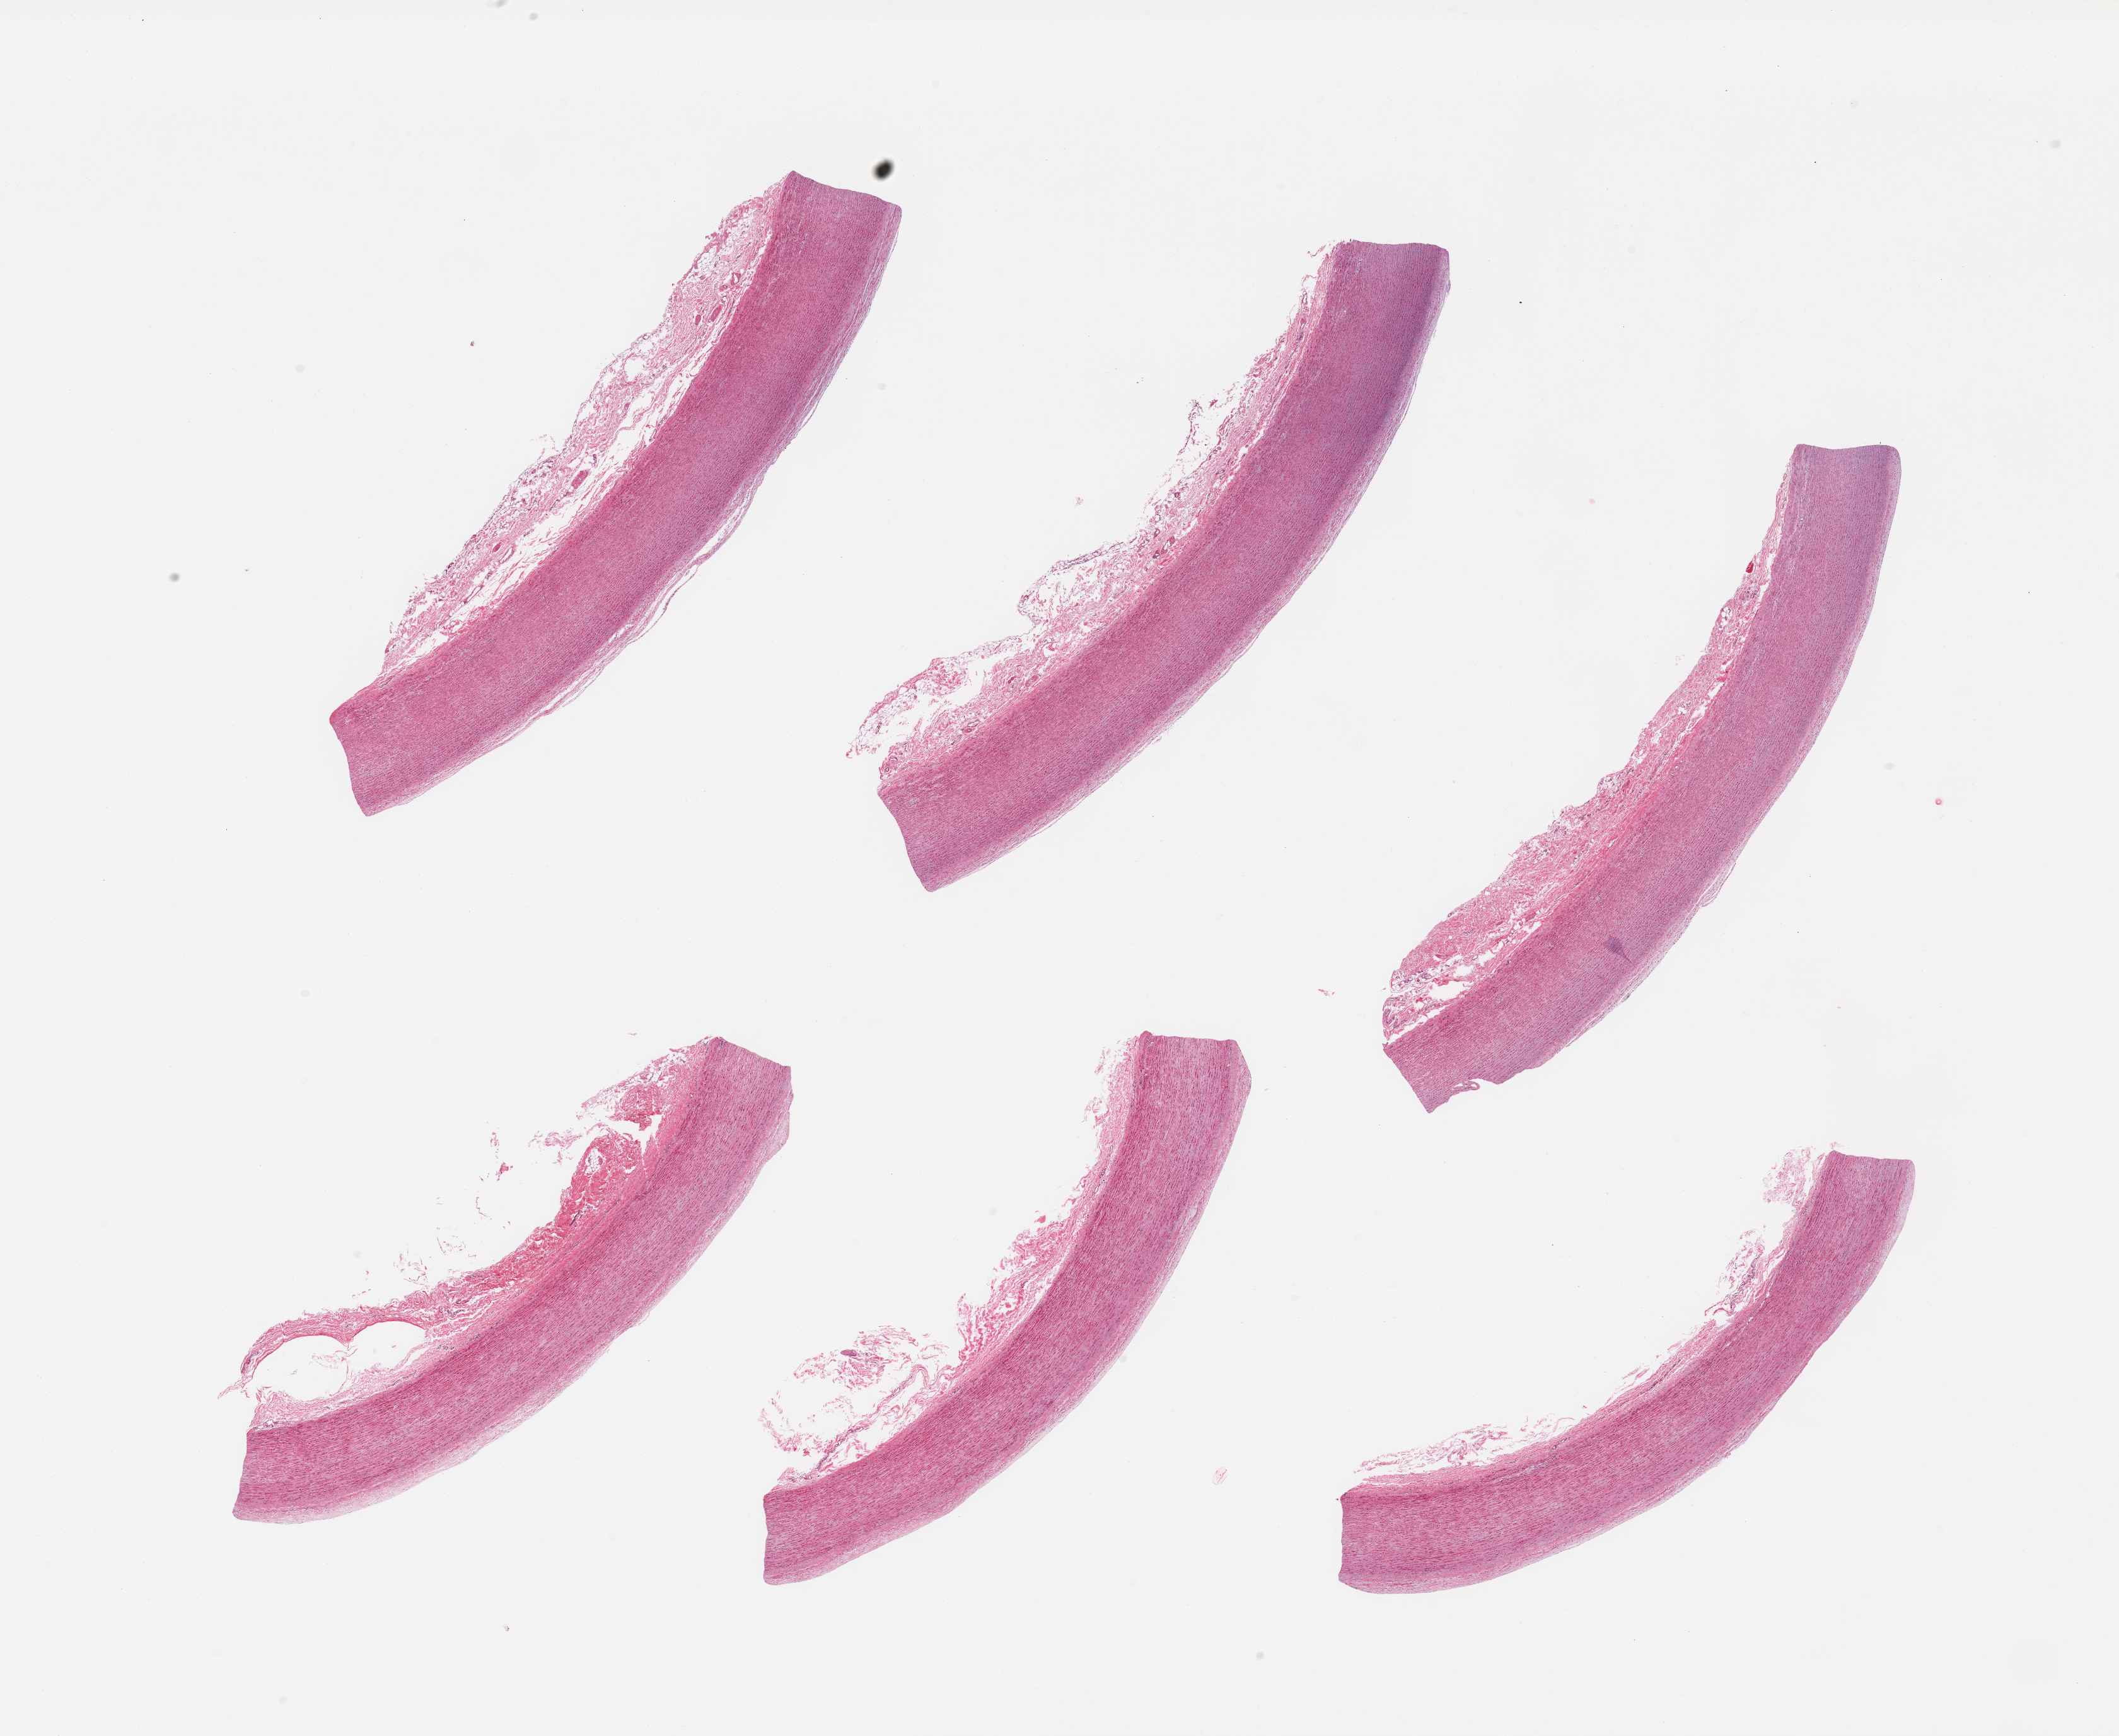
Digitized H&E-stained section, brightfield — low-resolution overview of the scanned area, about 26.6 x 21.8 mm. PAXgene-fixed paraffin-embedded (PFPE) section. Target tissue: aorta. Tissue donor sample. Female donor.
Pathologist's review note for this sample: 6 pieces, trace atherosis (up to ~0.2mm); adherent serosa up to ~1mm.